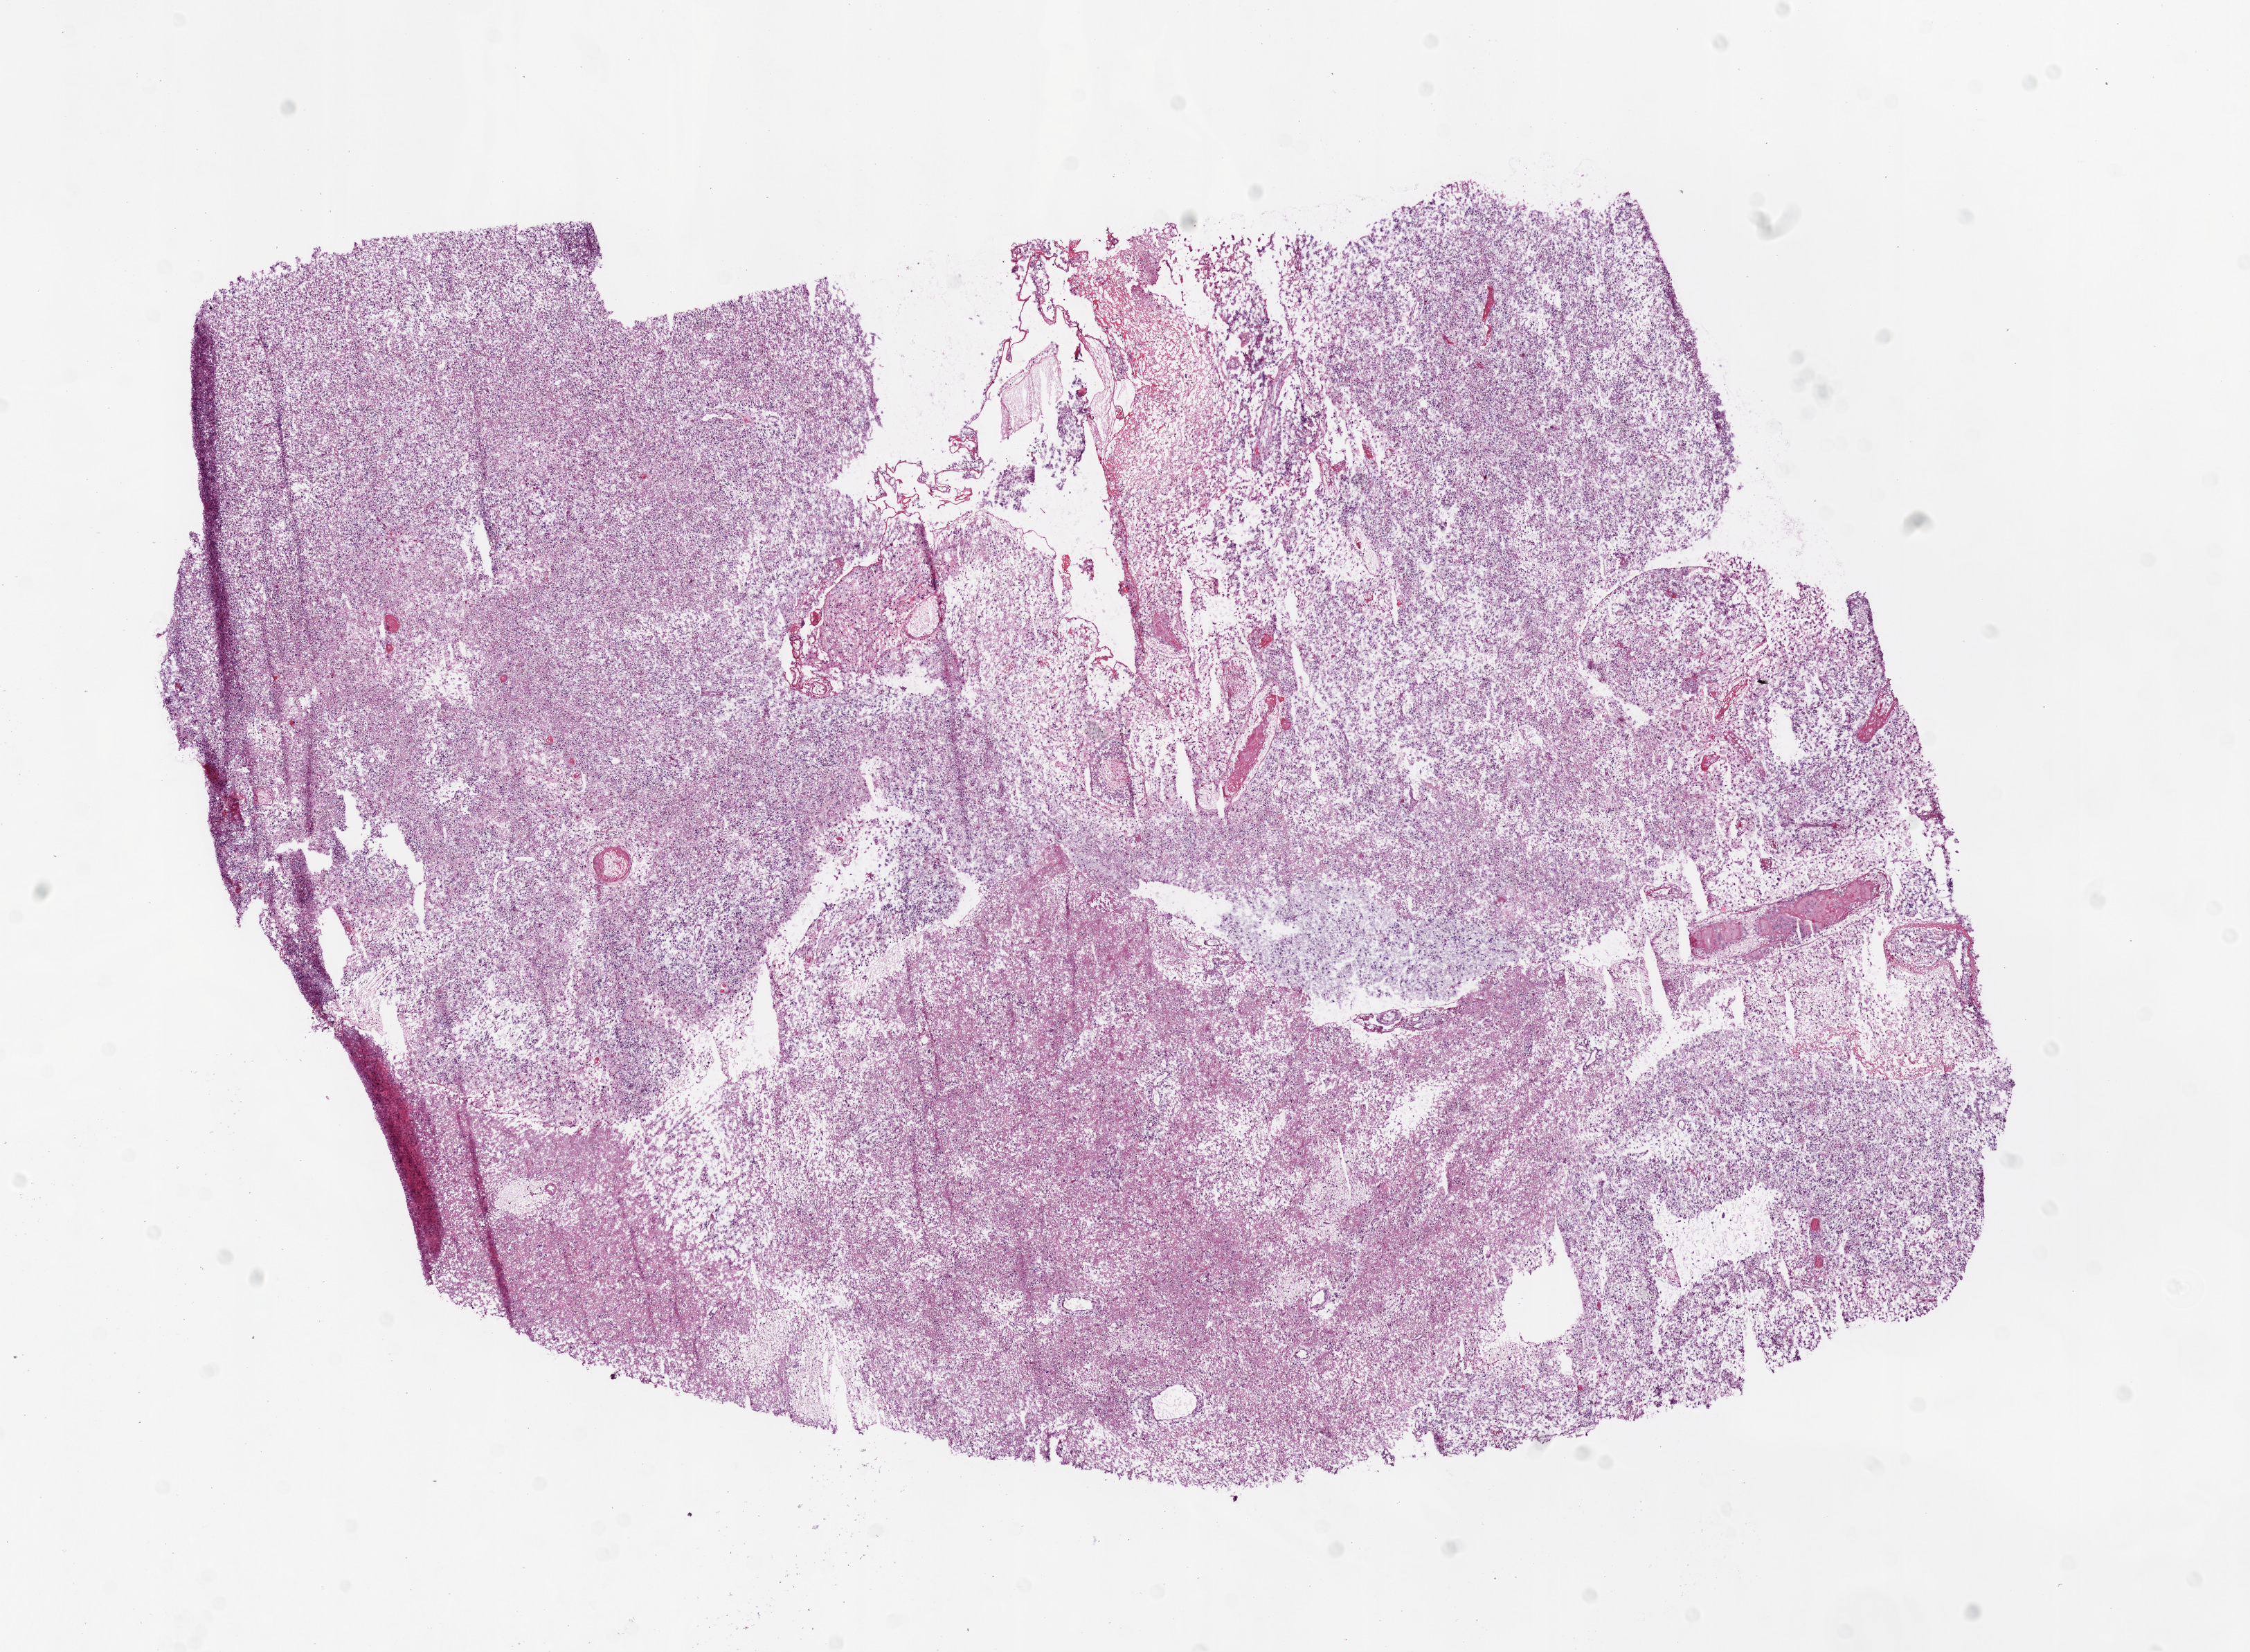
Digitized H&E tissue section (whole slide), whole scanned area (about 13.0 x 9.6 mm) shown as a low-resolution overview. Frozen section from the bottom of the tissue portion. Brain, primary tumour sample. Female, age 48 years at initial diagnosis.
Diagnosis: Glioblastoma.